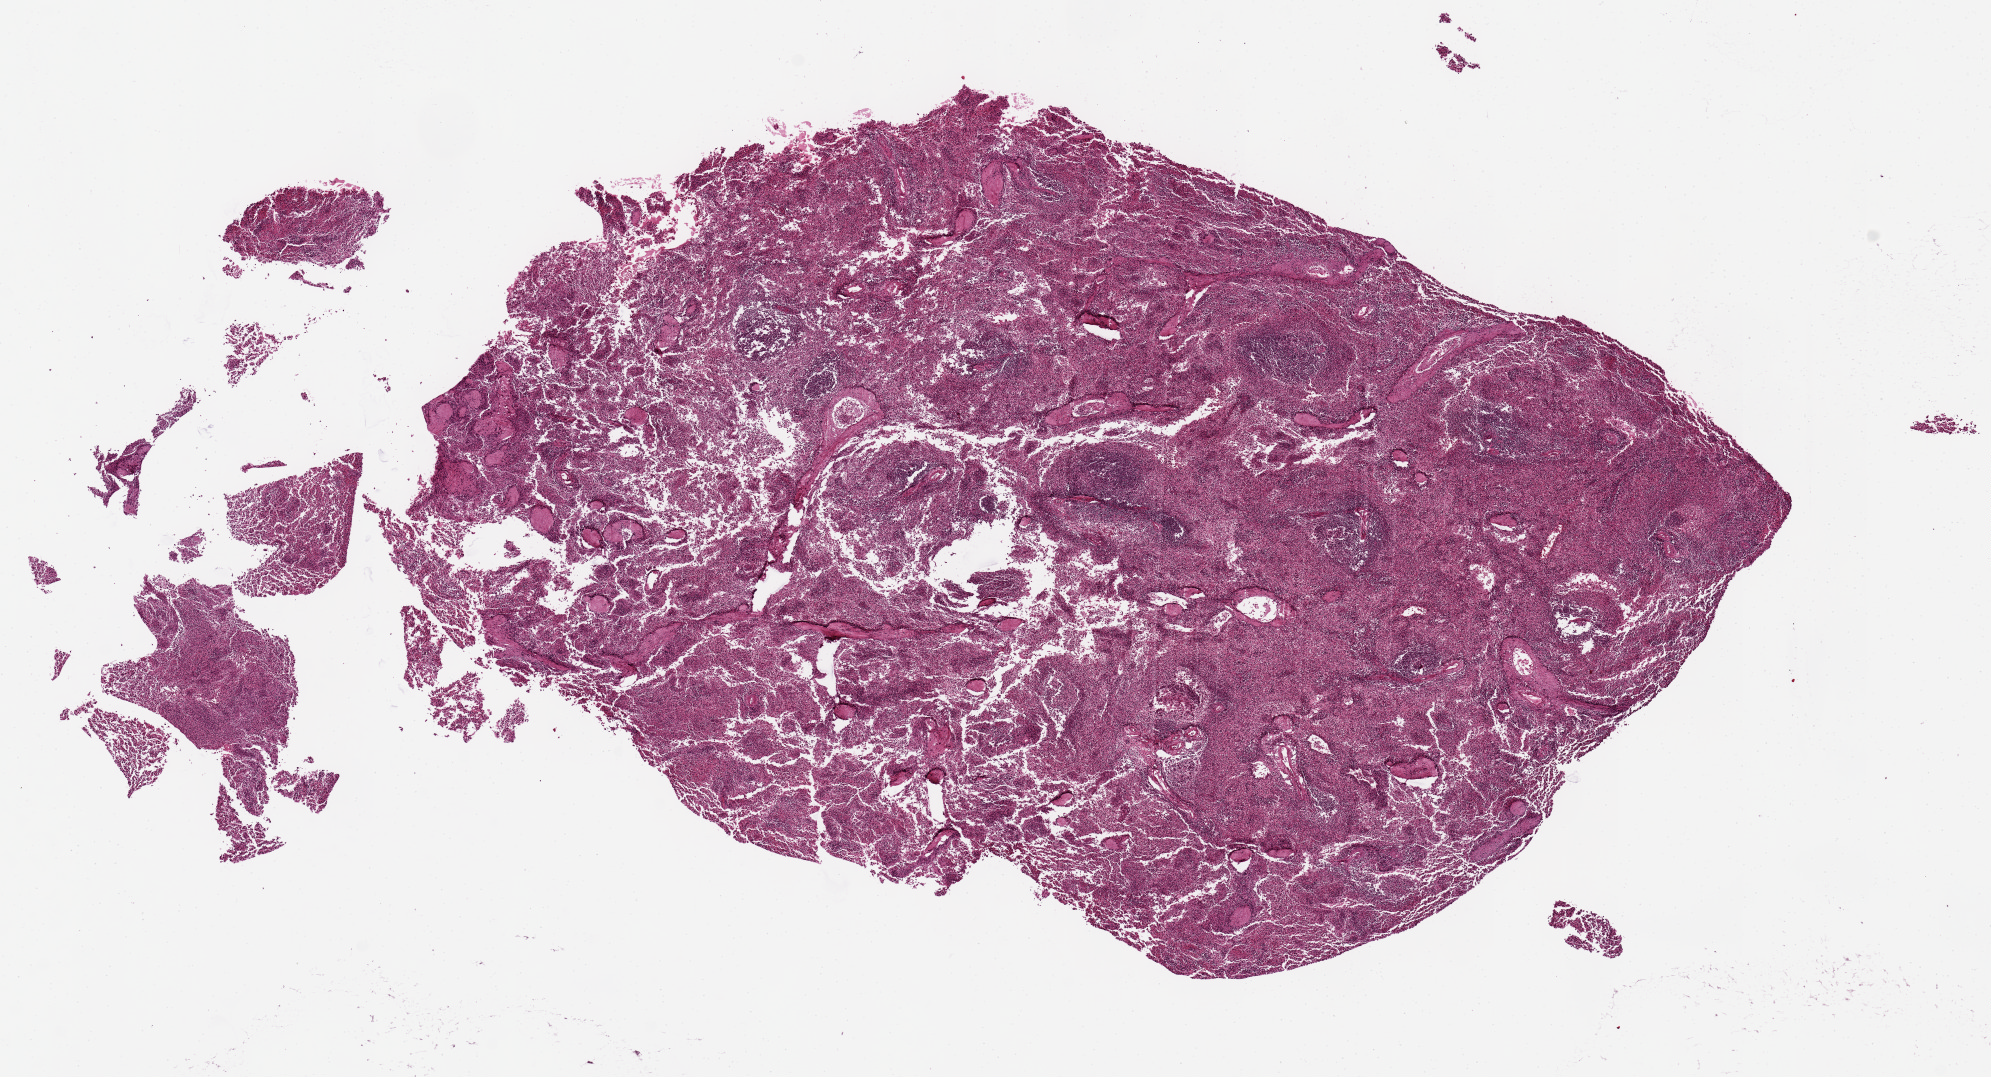
H&E whole-slide image, brightfield, low-resolution overview of the scanned area, about 15.8 x 8.5 mm (slide scanned at 20x), PAXgene-fixed, paraffin-embedded tissue, sampled site (target tissue): spleen, tissue donor sample.
- pathologist's review note for this sample: Poor fixation centrally